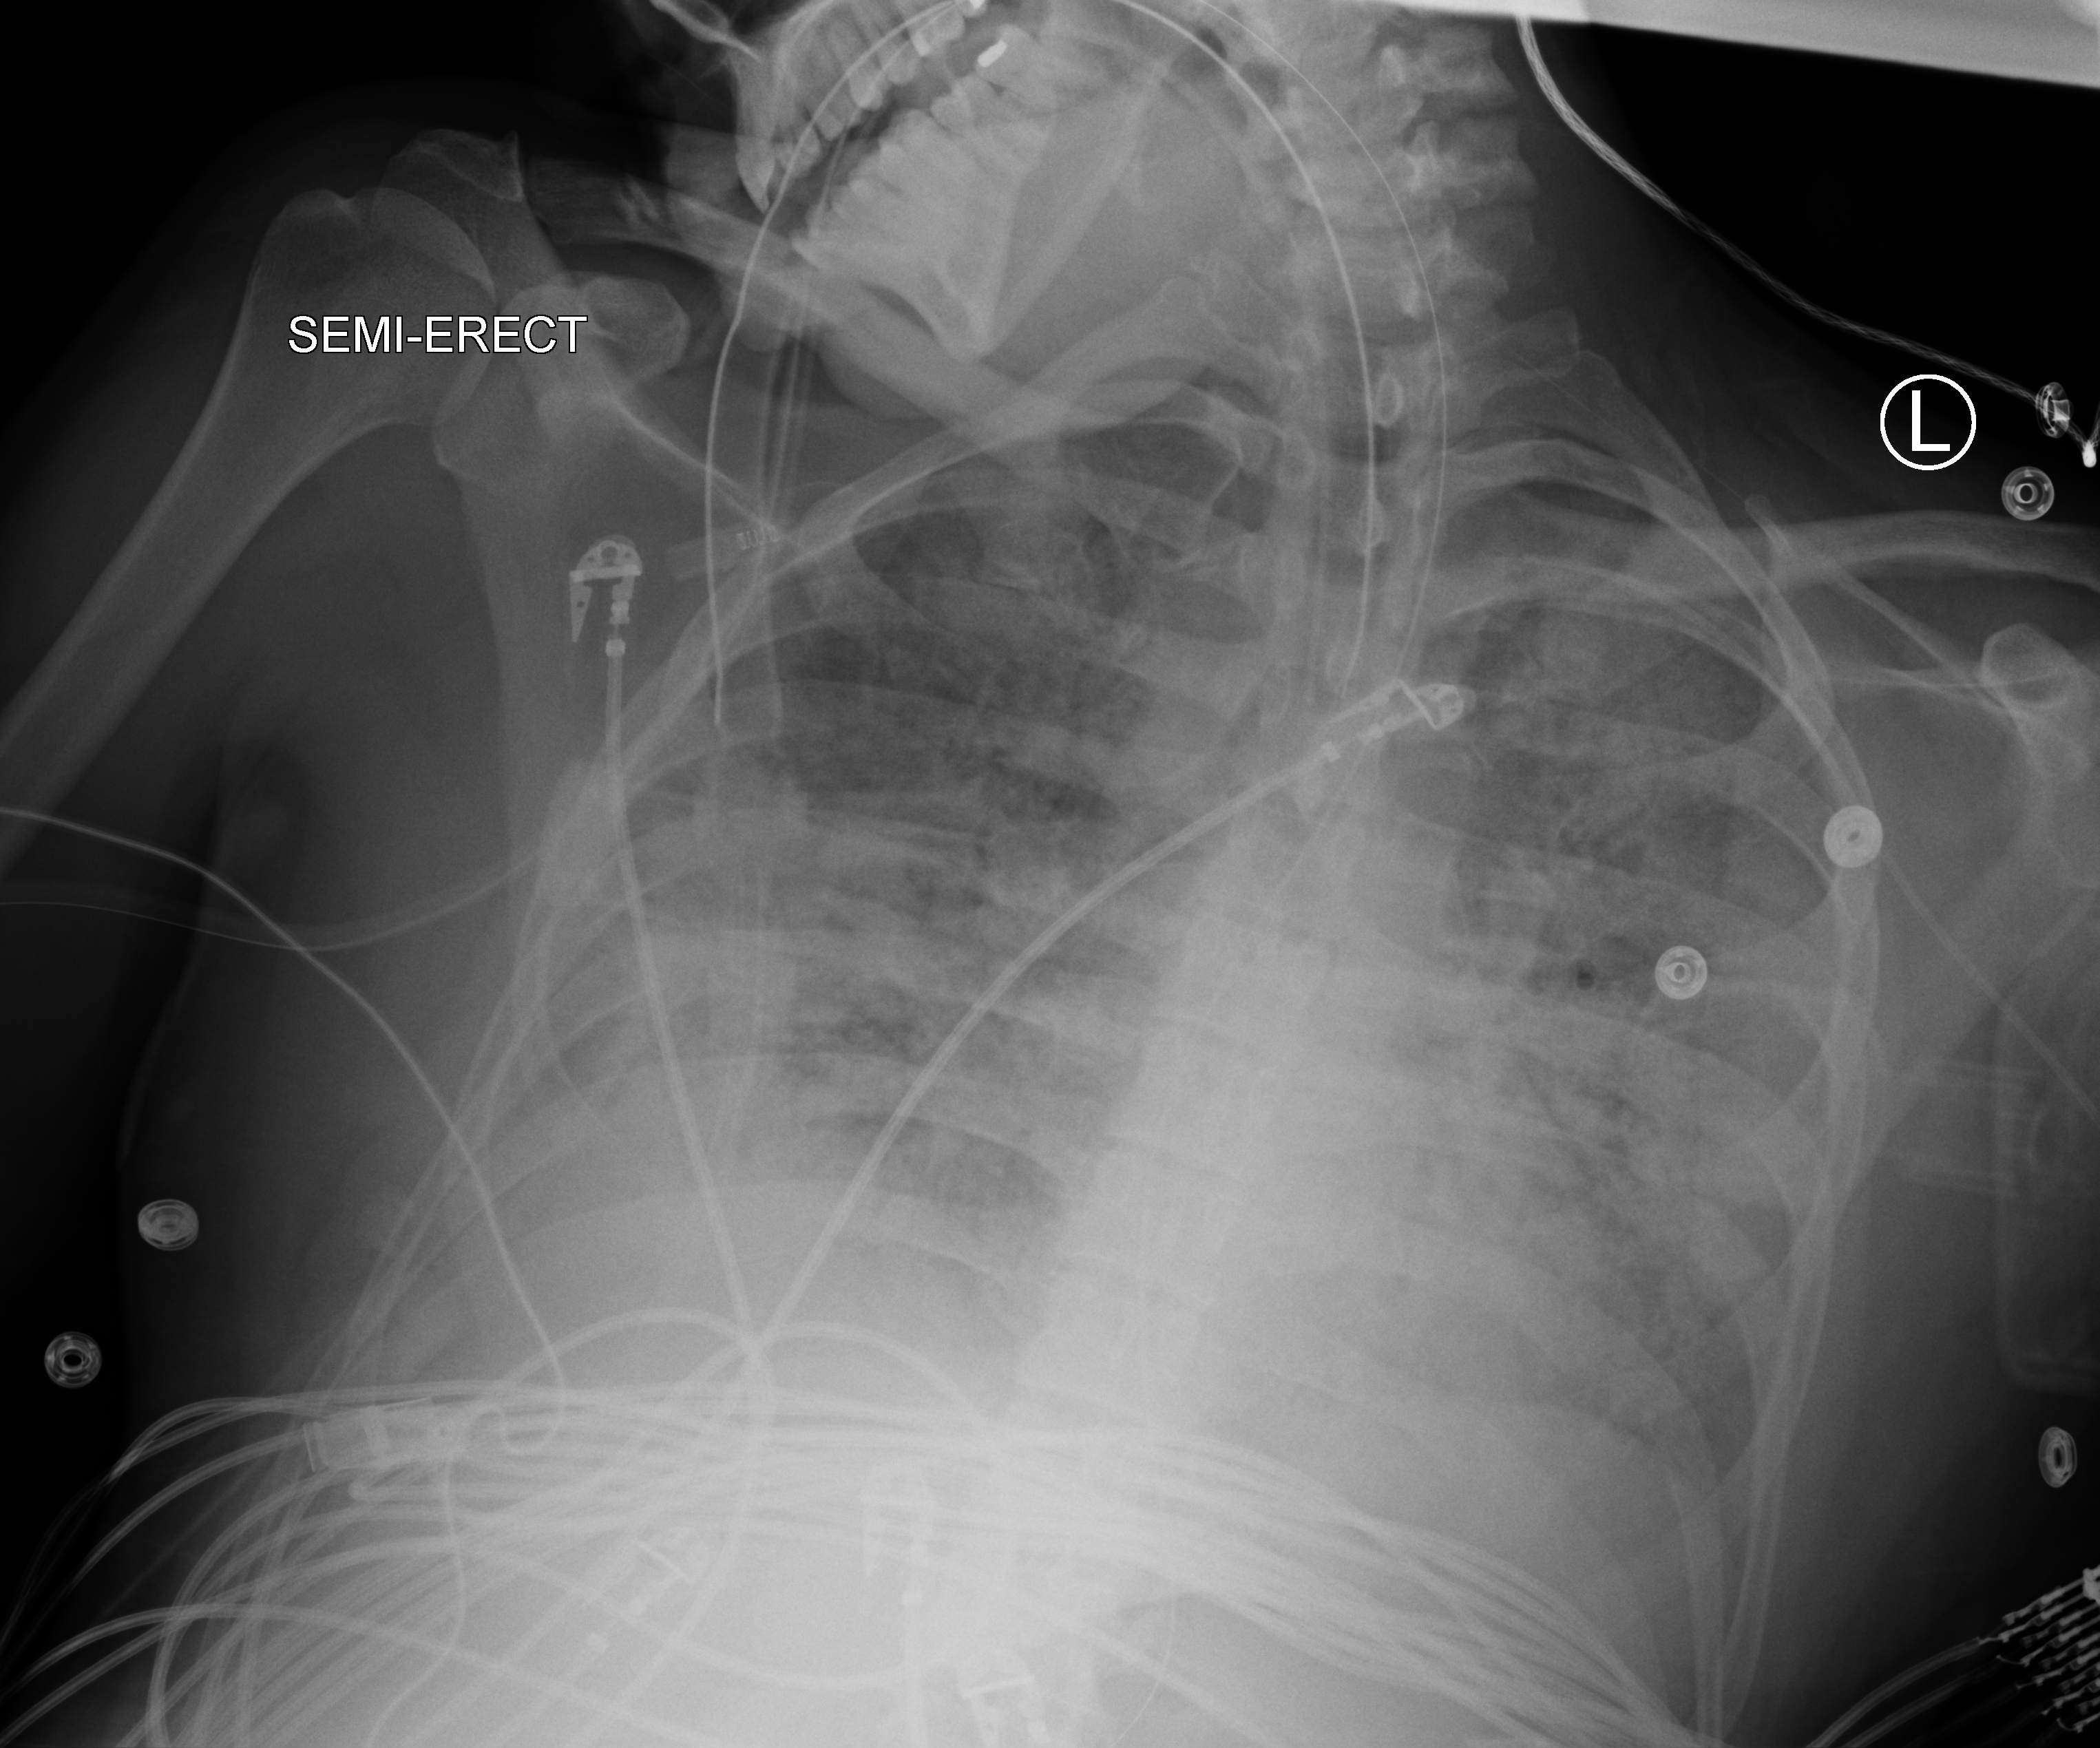
Portable chest radiograph, anteroposterior (AP) projection. Male patient hospitalised with COVID-19, age 18–59 years.
Admission-level facts for this patient (not findings on this image; timing relative to this image not recorded): length of hospital stay: 30 days; hypertension (admission record): no; mechanically ventilated during this hospital stay: yes.